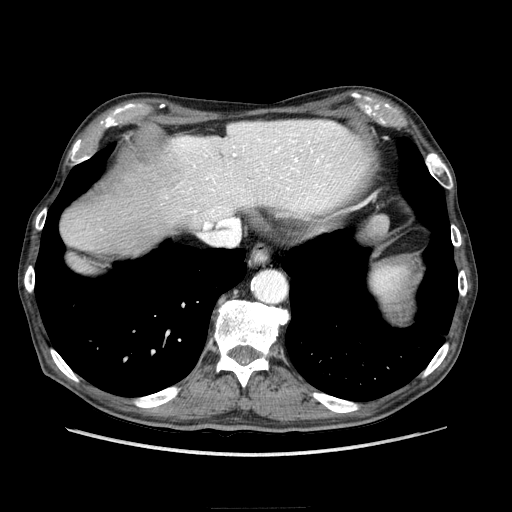
Contrast-enhanced abdominal CT (liver protocol), one axial slice; slice 189 of 218 in the series (ordered by position); 100 kVp; soft-tissue window (W 400 / L 40 HU); 2.5 mm slice thickness; 512 × 512 image matrix, field of view 380 × 380 mm. From the clinical record (not read from this slice): diagnosis: hepatocellular carcinoma (patient treated with transarterial chemoembolisation; whether this scan precedes or follows treatment is not stated here); TNM stage (as recorded): Stage-IIIA; Child-Pugh class: A; tumour differentiation: well differentiated.
Annotated regions visible in this slice (semi-automatically segmented with operator editing):
- liver parenchyma outside the tumour (the mass and vessels are separate outlines, so this box may not span the whole liver): bounding box [x1, y1, x2, y2] px = [114, 120, 368, 254]
- liver vessels: [166, 122, 354, 220]